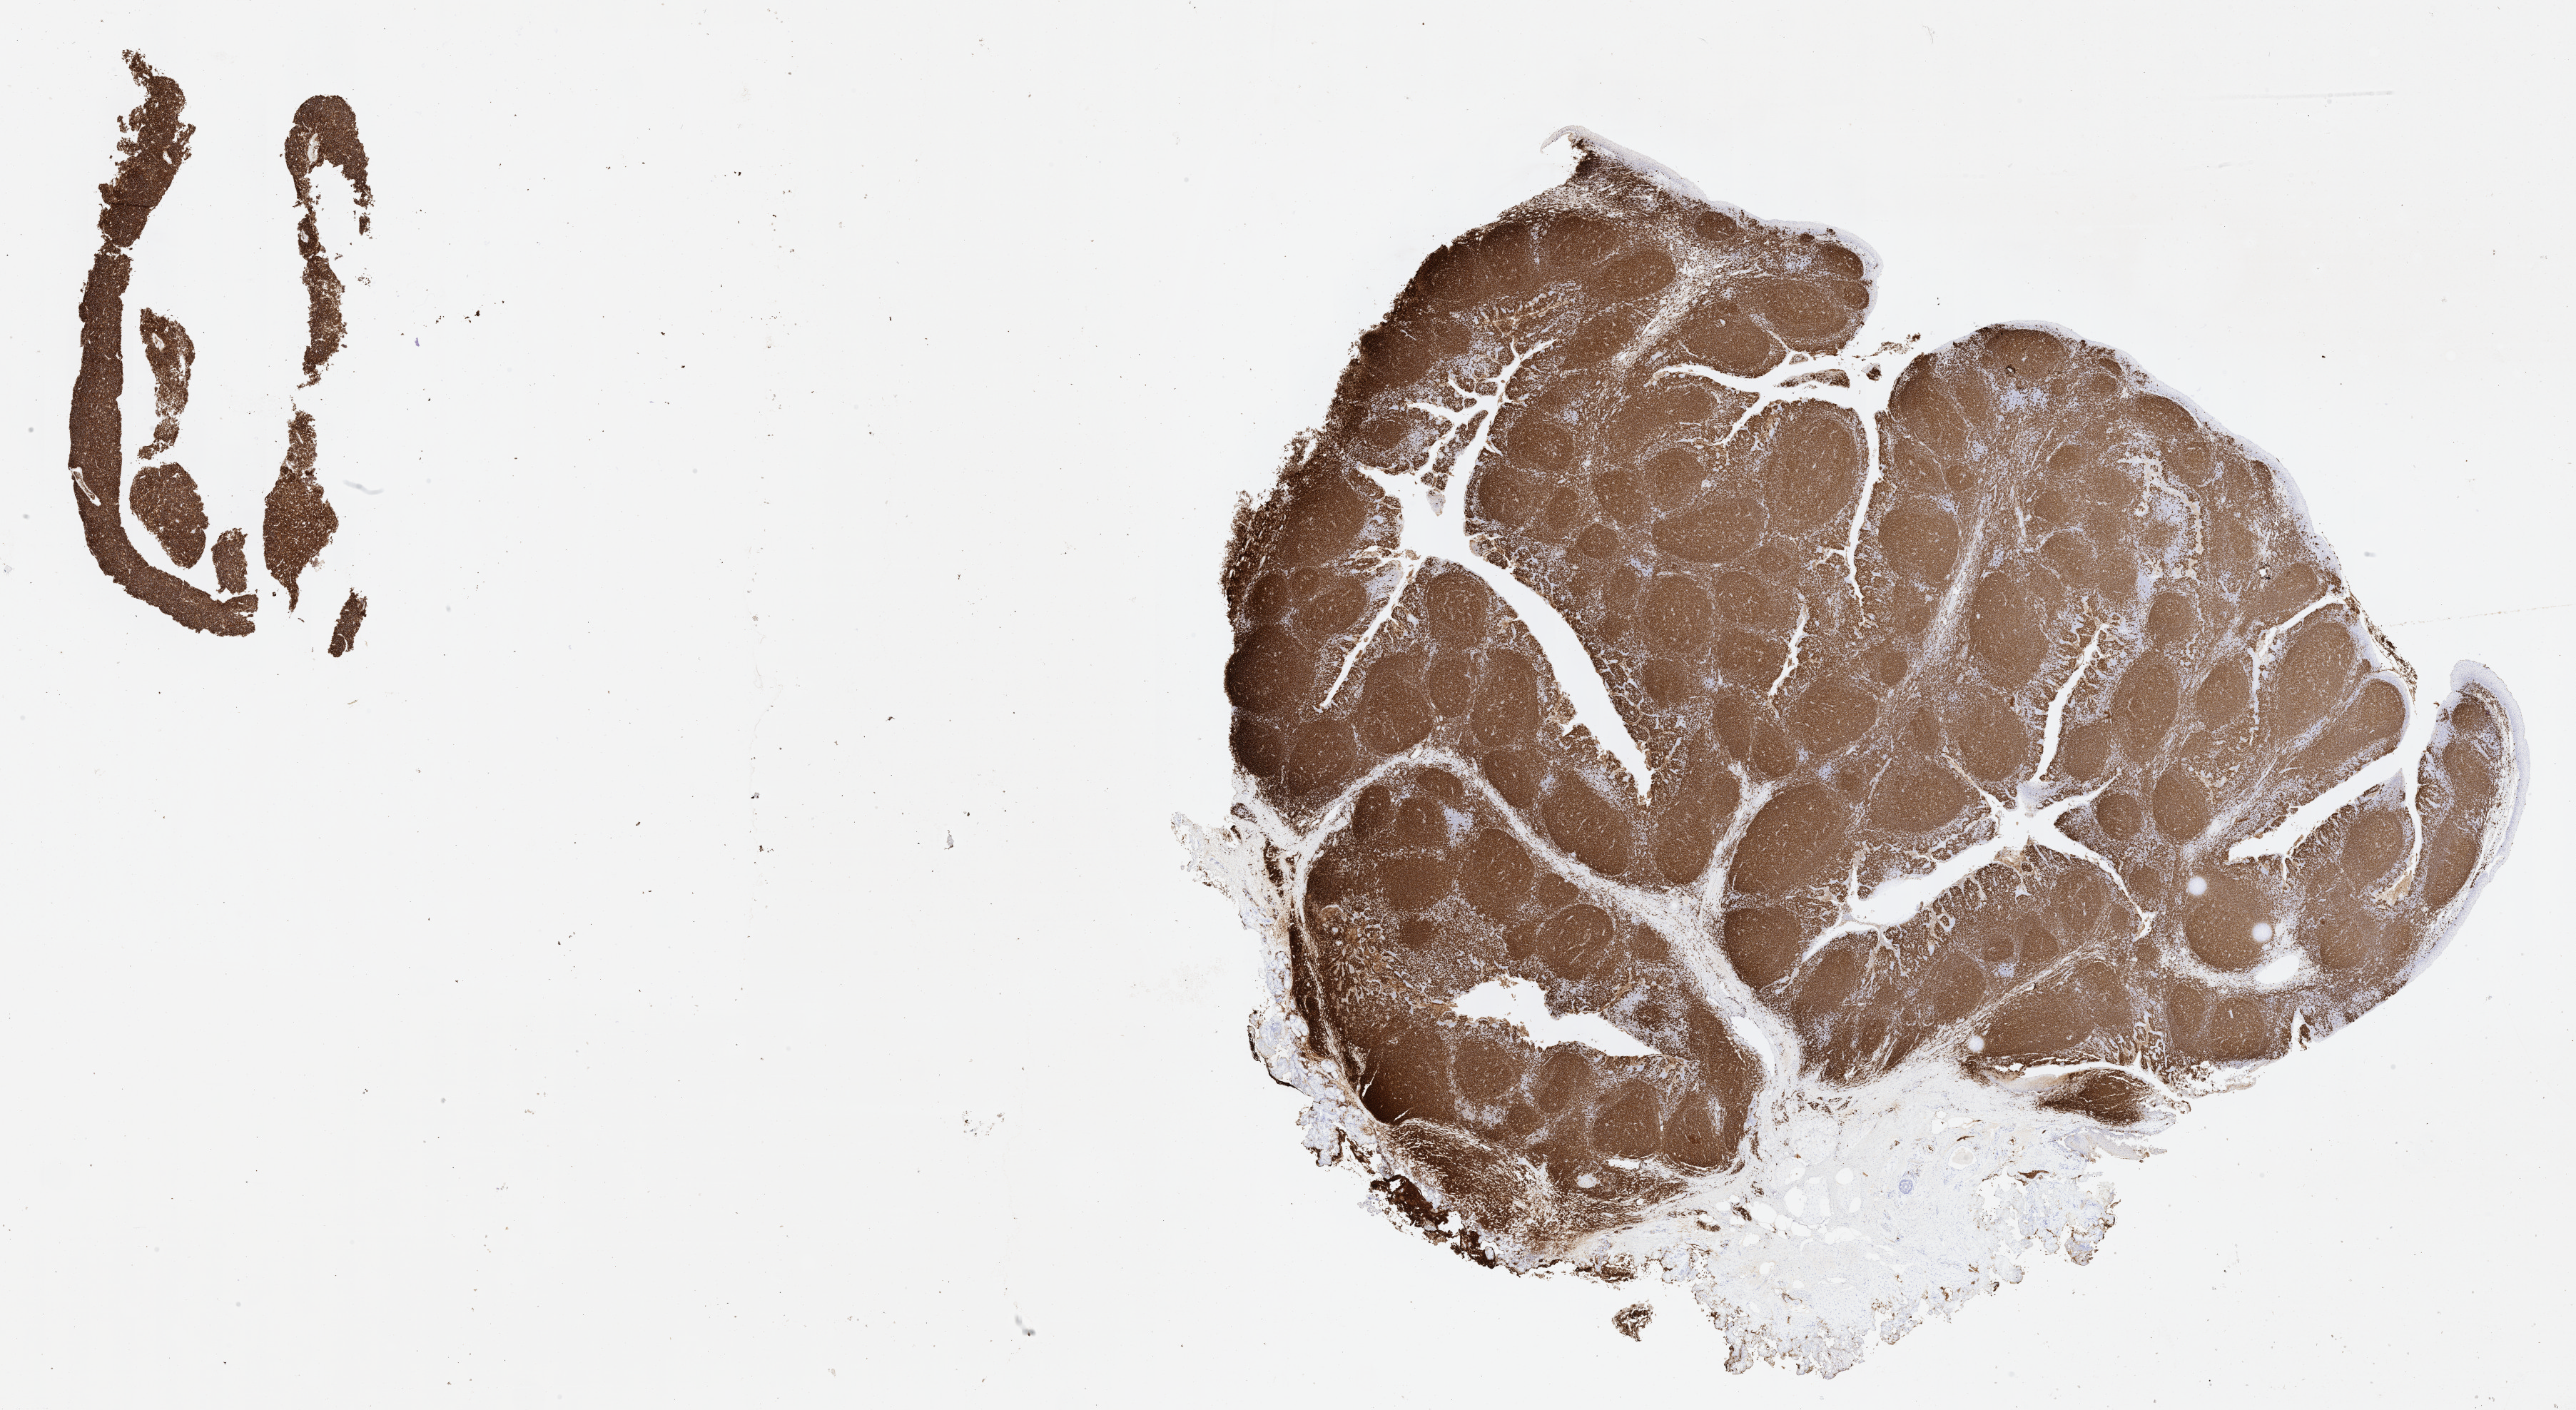
Whole-slide image, immunohistochemical stain for CD20, shown as a low-resolution overview of the whole scanned area (about 29.2 x 16.0 mm), specimen: tumor tissue. Patient female; age 10 years.
Histologic diagnosis: Burkitt lymphoma, NOS.